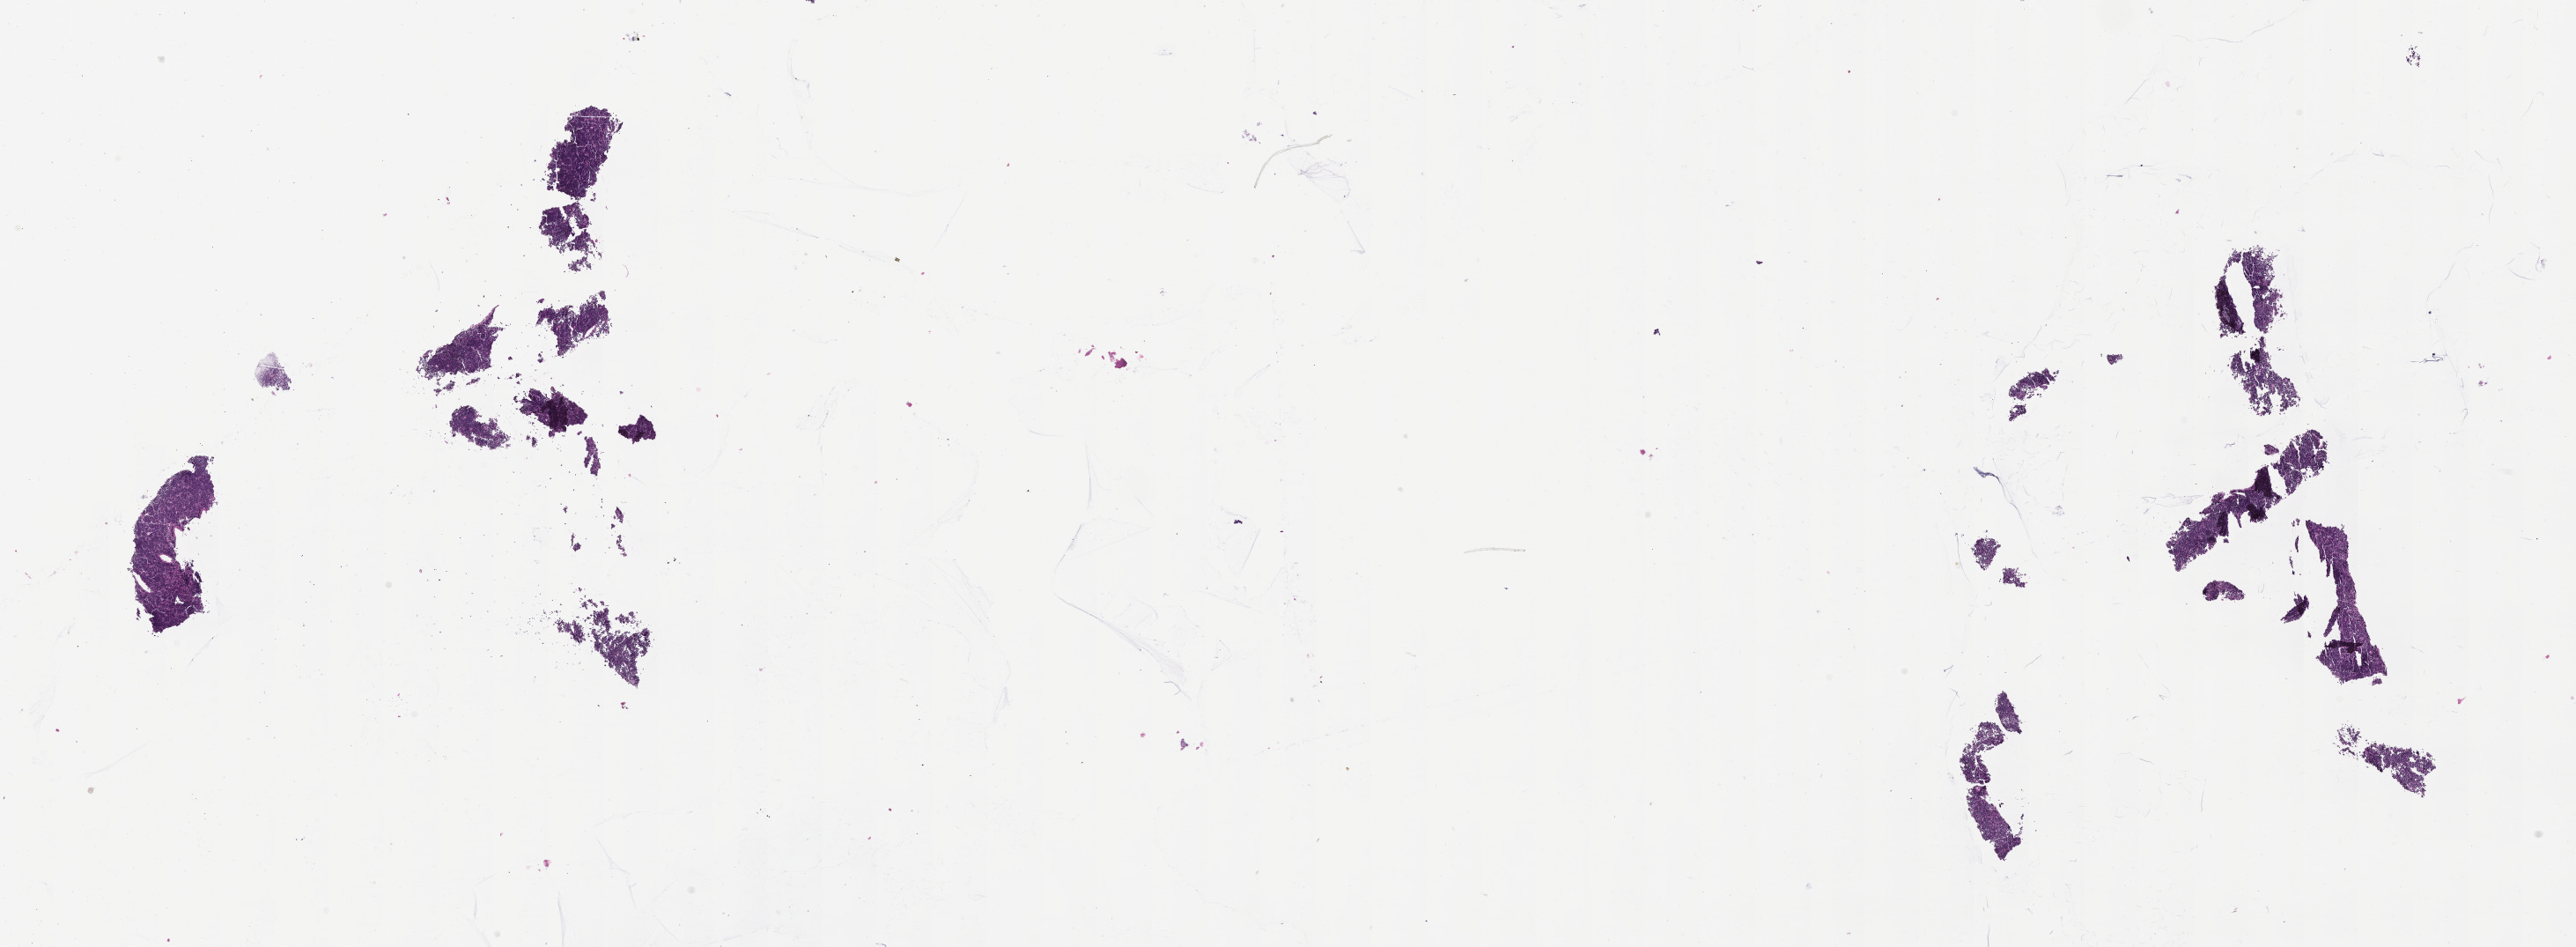
Hematoxylin and eosin (H&E) whole-slide image — low-resolution overview of the scanned area, about 23.6 x 8.7 mm. Specimen: tumor tissue. Anatomic site: peritoneum. Patient: female, age at initial diagnosis 6 years.
- diagnosis: Burkitt lymphoma, NOS